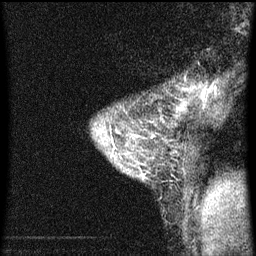
Breast MRI (dynamic contrast-enhanced), one sagittal slice. Position 51 of 60 along the scan axis. Dynamic contrast-enhanced series, image 2 of 3 at this slice position (ordered by acquisition). 1.5 T. TE 4.2 ms, TR 8 ms. 2 mm slice thickness. 256 × 256 image matrix, field of view 180 × 180 mm. Patient: female, 33 years.
Annotated regions visible in this slice (semi-automatically segmented with operator editing):
- analysis volume of interest (the breast-tissue region the enhancement analysis was run in; not a lesion): bounding box [x1, y1, x2, y2] px = [93, 82, 195, 205]
- tumour enhancement mask (voxels above the 70 % enhancement threshold inside the analysis volume of interest): [135, 136, 139, 137]